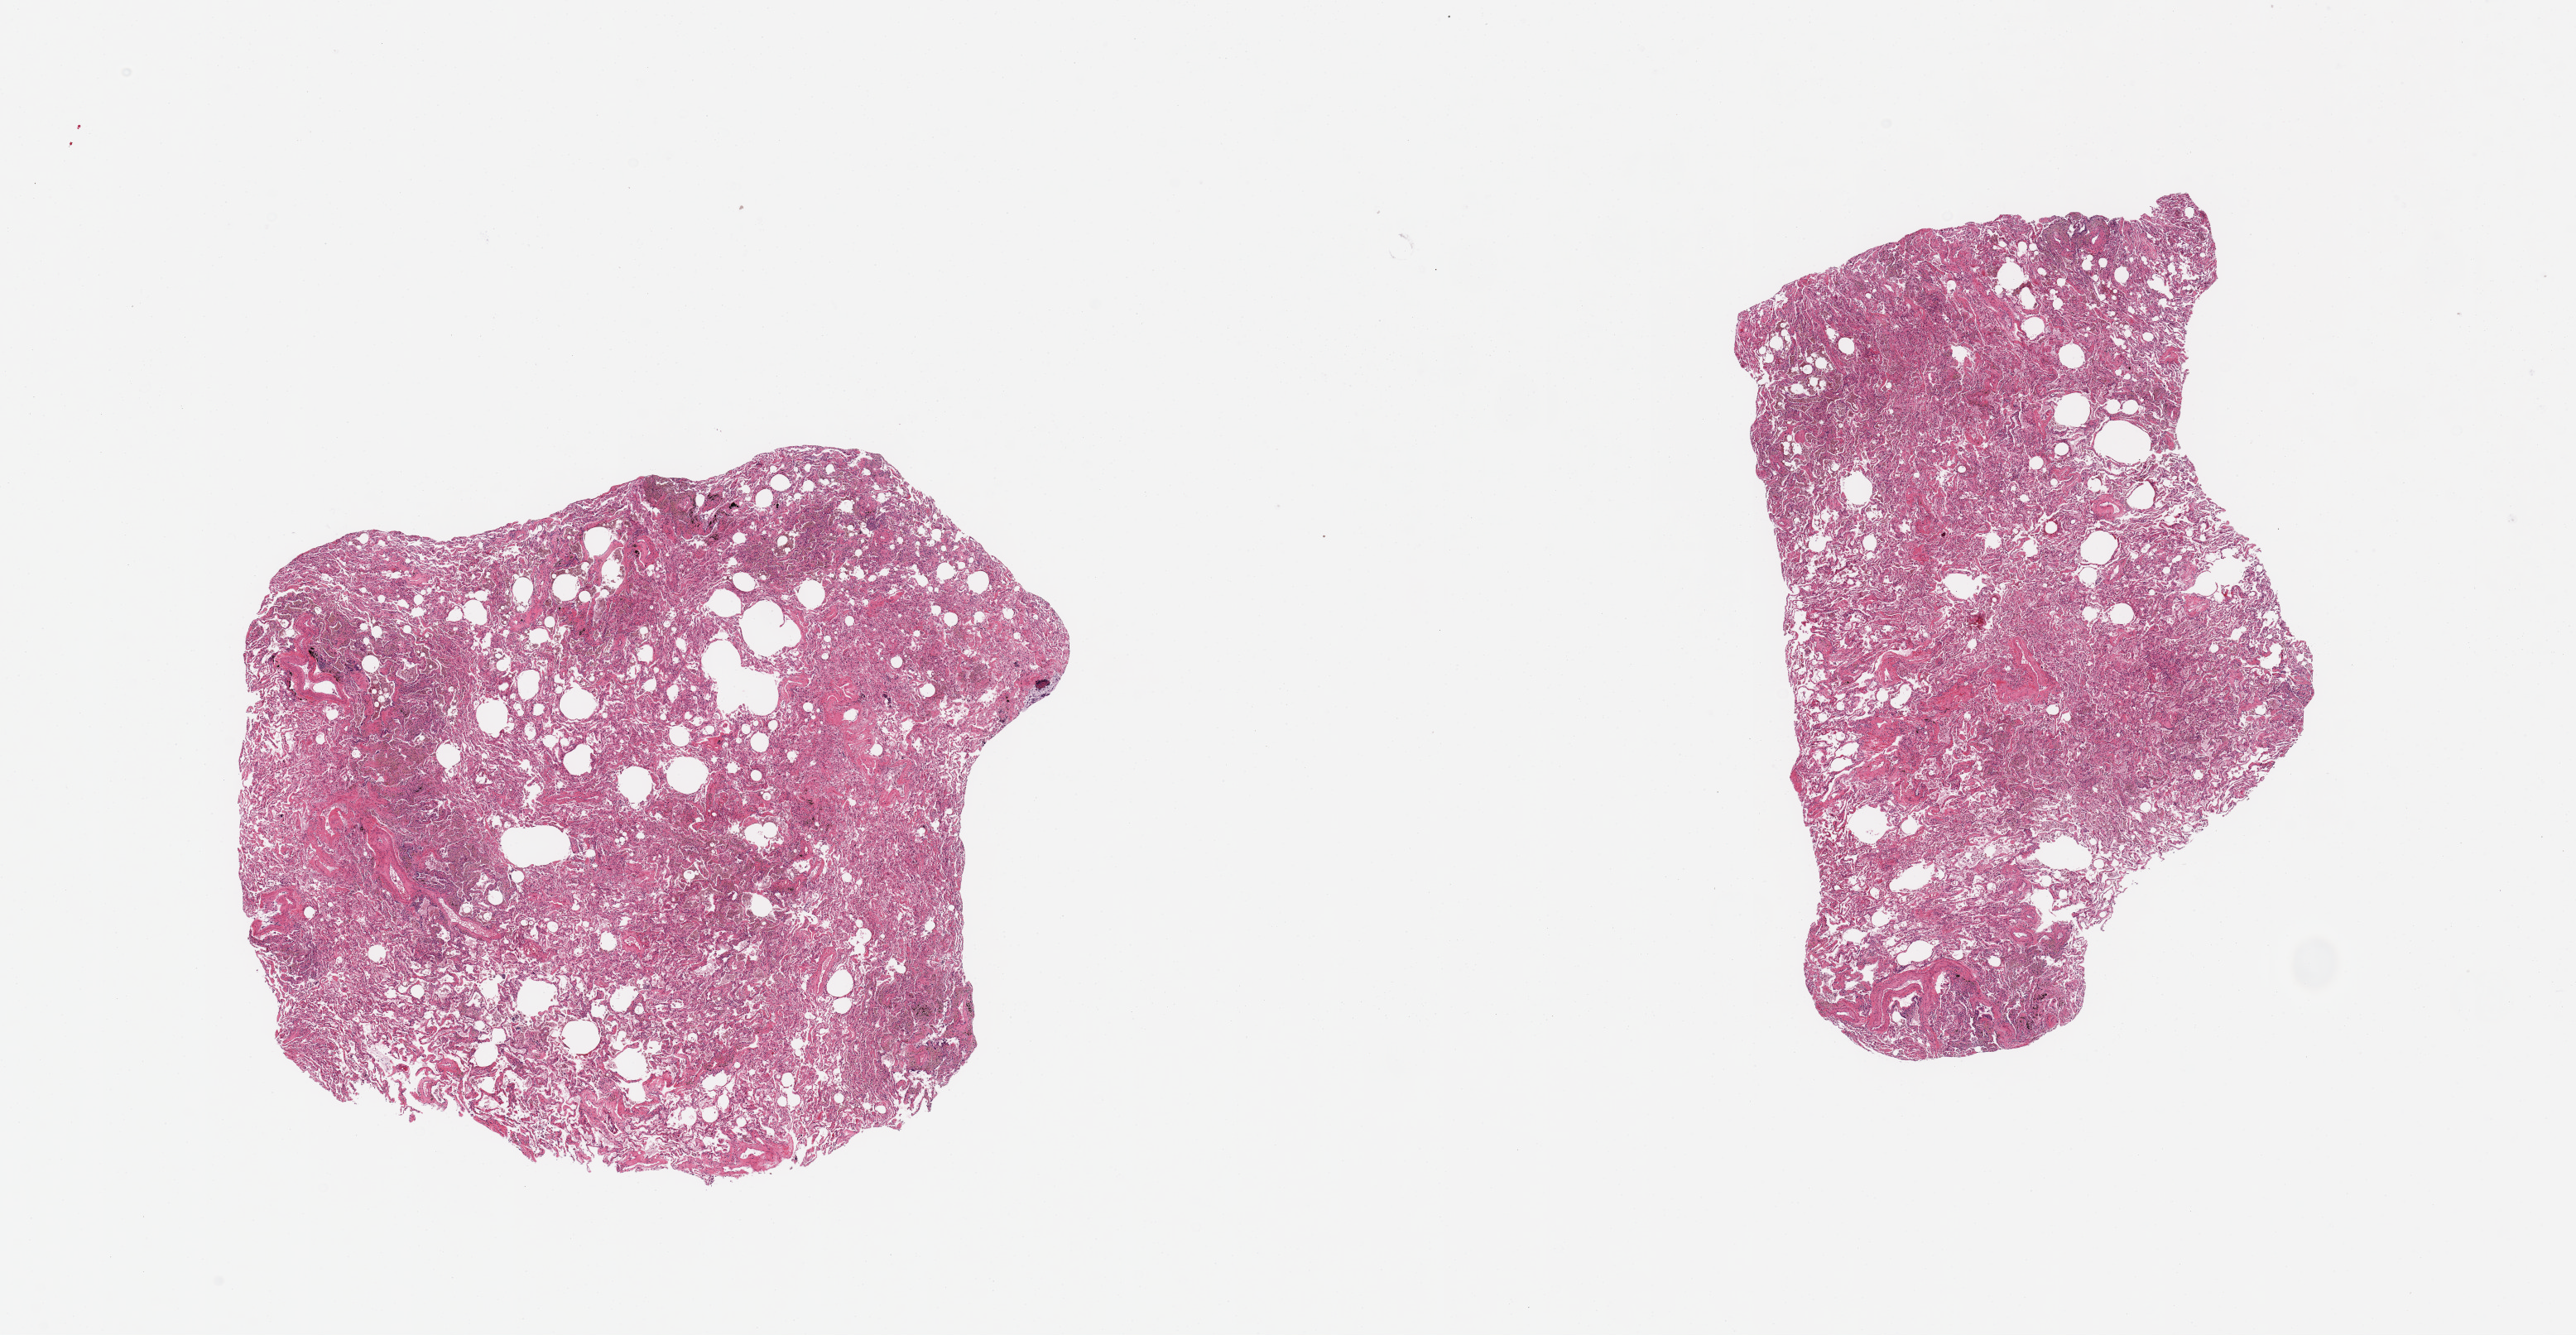
H&E whole-slide image — whole scanned area (about 24.6 x 12.8 mm, acquisition: 20x scan) shown as a low-resolution overview; PAXgene-fixed paraffin-embedded (PFPE) section; section of lung (target tissue); donor tissue sample. Donor: male.
Reviewer comment on this tissue sample: 2 pieces, mild edema, evidence of chronic congestion, hemosiderin-laden macrophages moderately abundant.